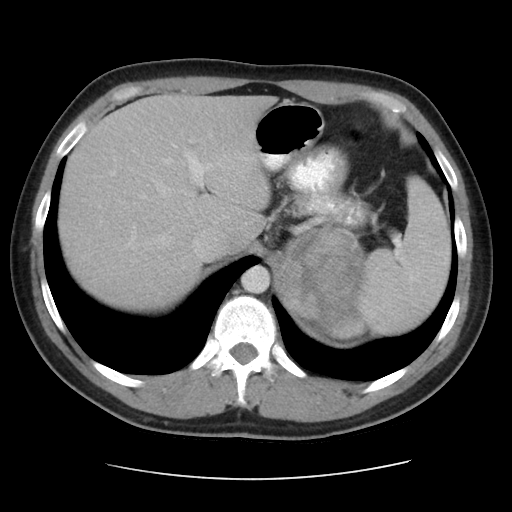
Contrast-enhanced abdominal CT, one axial slice; slice 35 of 48 in the series (ordered by position); reconstruction kernel STANDARD; 120 kVp; intravenous contrast given; soft-tissue window (W 400 / L 40 HU); 512 × 512 image matrix. Patient: male, 32 years. Case-level facts recorded for this patient, not image findings: diagnosis: adrenocortical carcinoma; tumour side: left adrenal; tumour size at pathology: 14 cm; Ki-67 index: 67 %; stage (as recorded): 3.
Outlined on this slice (semi-automatic segmentation, software-assisted and operator-edited):
- mass: bounding box [x1, y1, x2, y2] px = [286, 231, 365, 336]